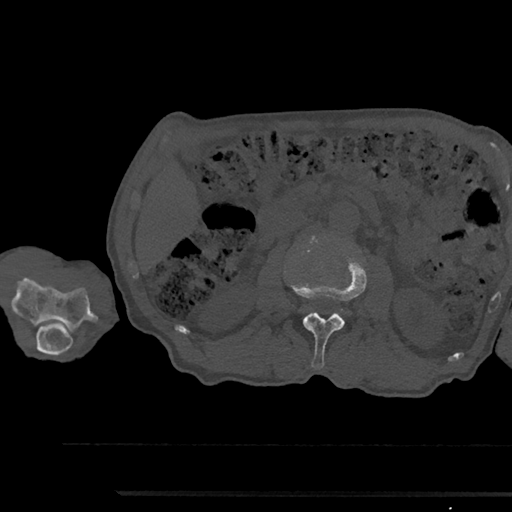
CT including the spine, one axial slice. Slice 545 of 797 in the series (ordered by position). 120 kVp. Bone window (W 1800 / L 400 HU). 0.5 mm slice thickness. 512 × 512 image matrix. Male patient, age 79 years. From the clinical record (not read from this slice): primary cancer: prostate.
Structures marked on this image (semi-automatic segmentation, software-assisted and operator-edited):
- L2 vertebra: box from (x=291, y=246) to (x=366, y=368) px